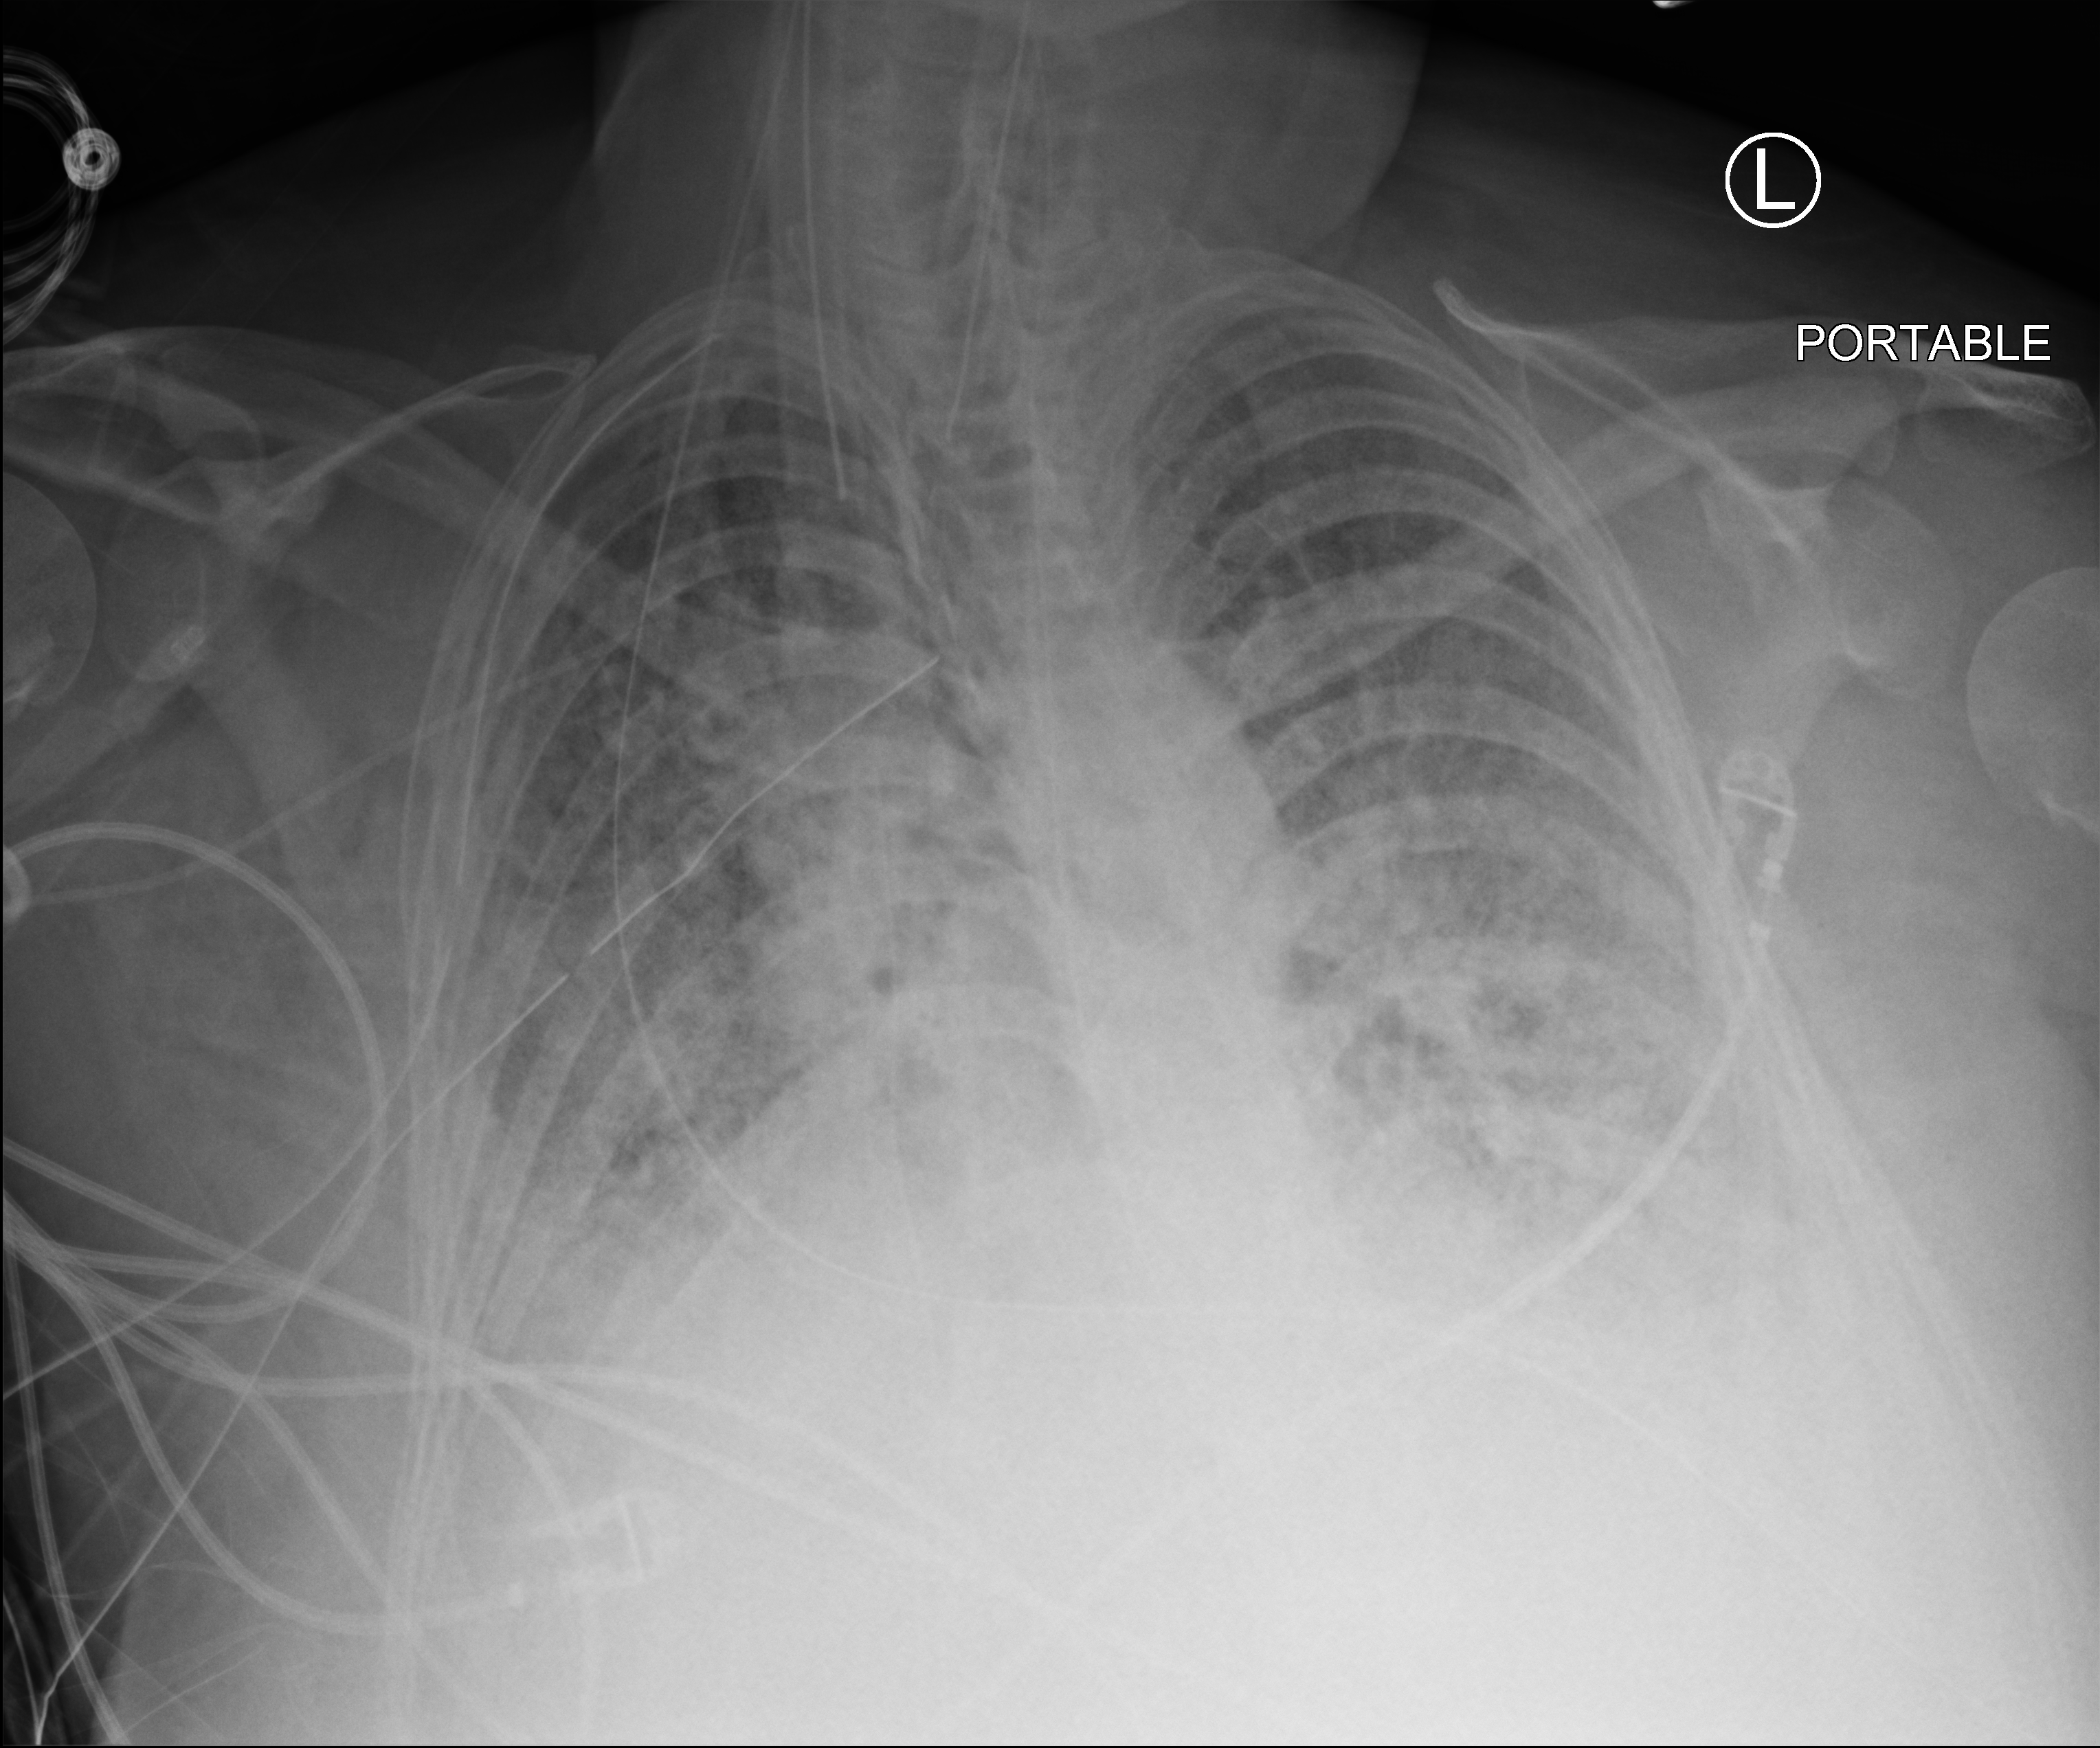
Portable chest radiograph, anteroposterior (AP) projection. Adult patient hospitalised with COVID-19, age 18–59 years.
Hospital-stay facts (about this admission, not read from this image; timing relative to this image not recorded):
- chronic kidney disease (admission record): no
- COPD (admission record): no
- mechanically ventilated during this hospital stay: yes